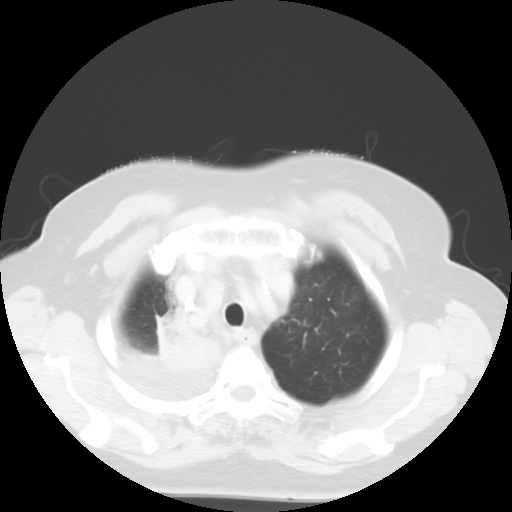
Chest CT, one axial slice. Slice 45 of 52 in the series (ordered by position). Reconstruction kernel STANDARD. Lung window (W 1500 / L -600 HU). 512 × 512 image matrix, field of view 333 × 333 mm. Female patient, age 81 years. Case-level facts recorded for this patient, not image findings: clinical TNM (as recorded): T4 N3 M1b.
Annotated regions visible in this slice (bounding box drawn by a radiologist):
- lung tumour (recorded histology: adenocarcinoma): bounding box (x1, y1, x2, y2) in pixels: (148, 315, 225, 375)